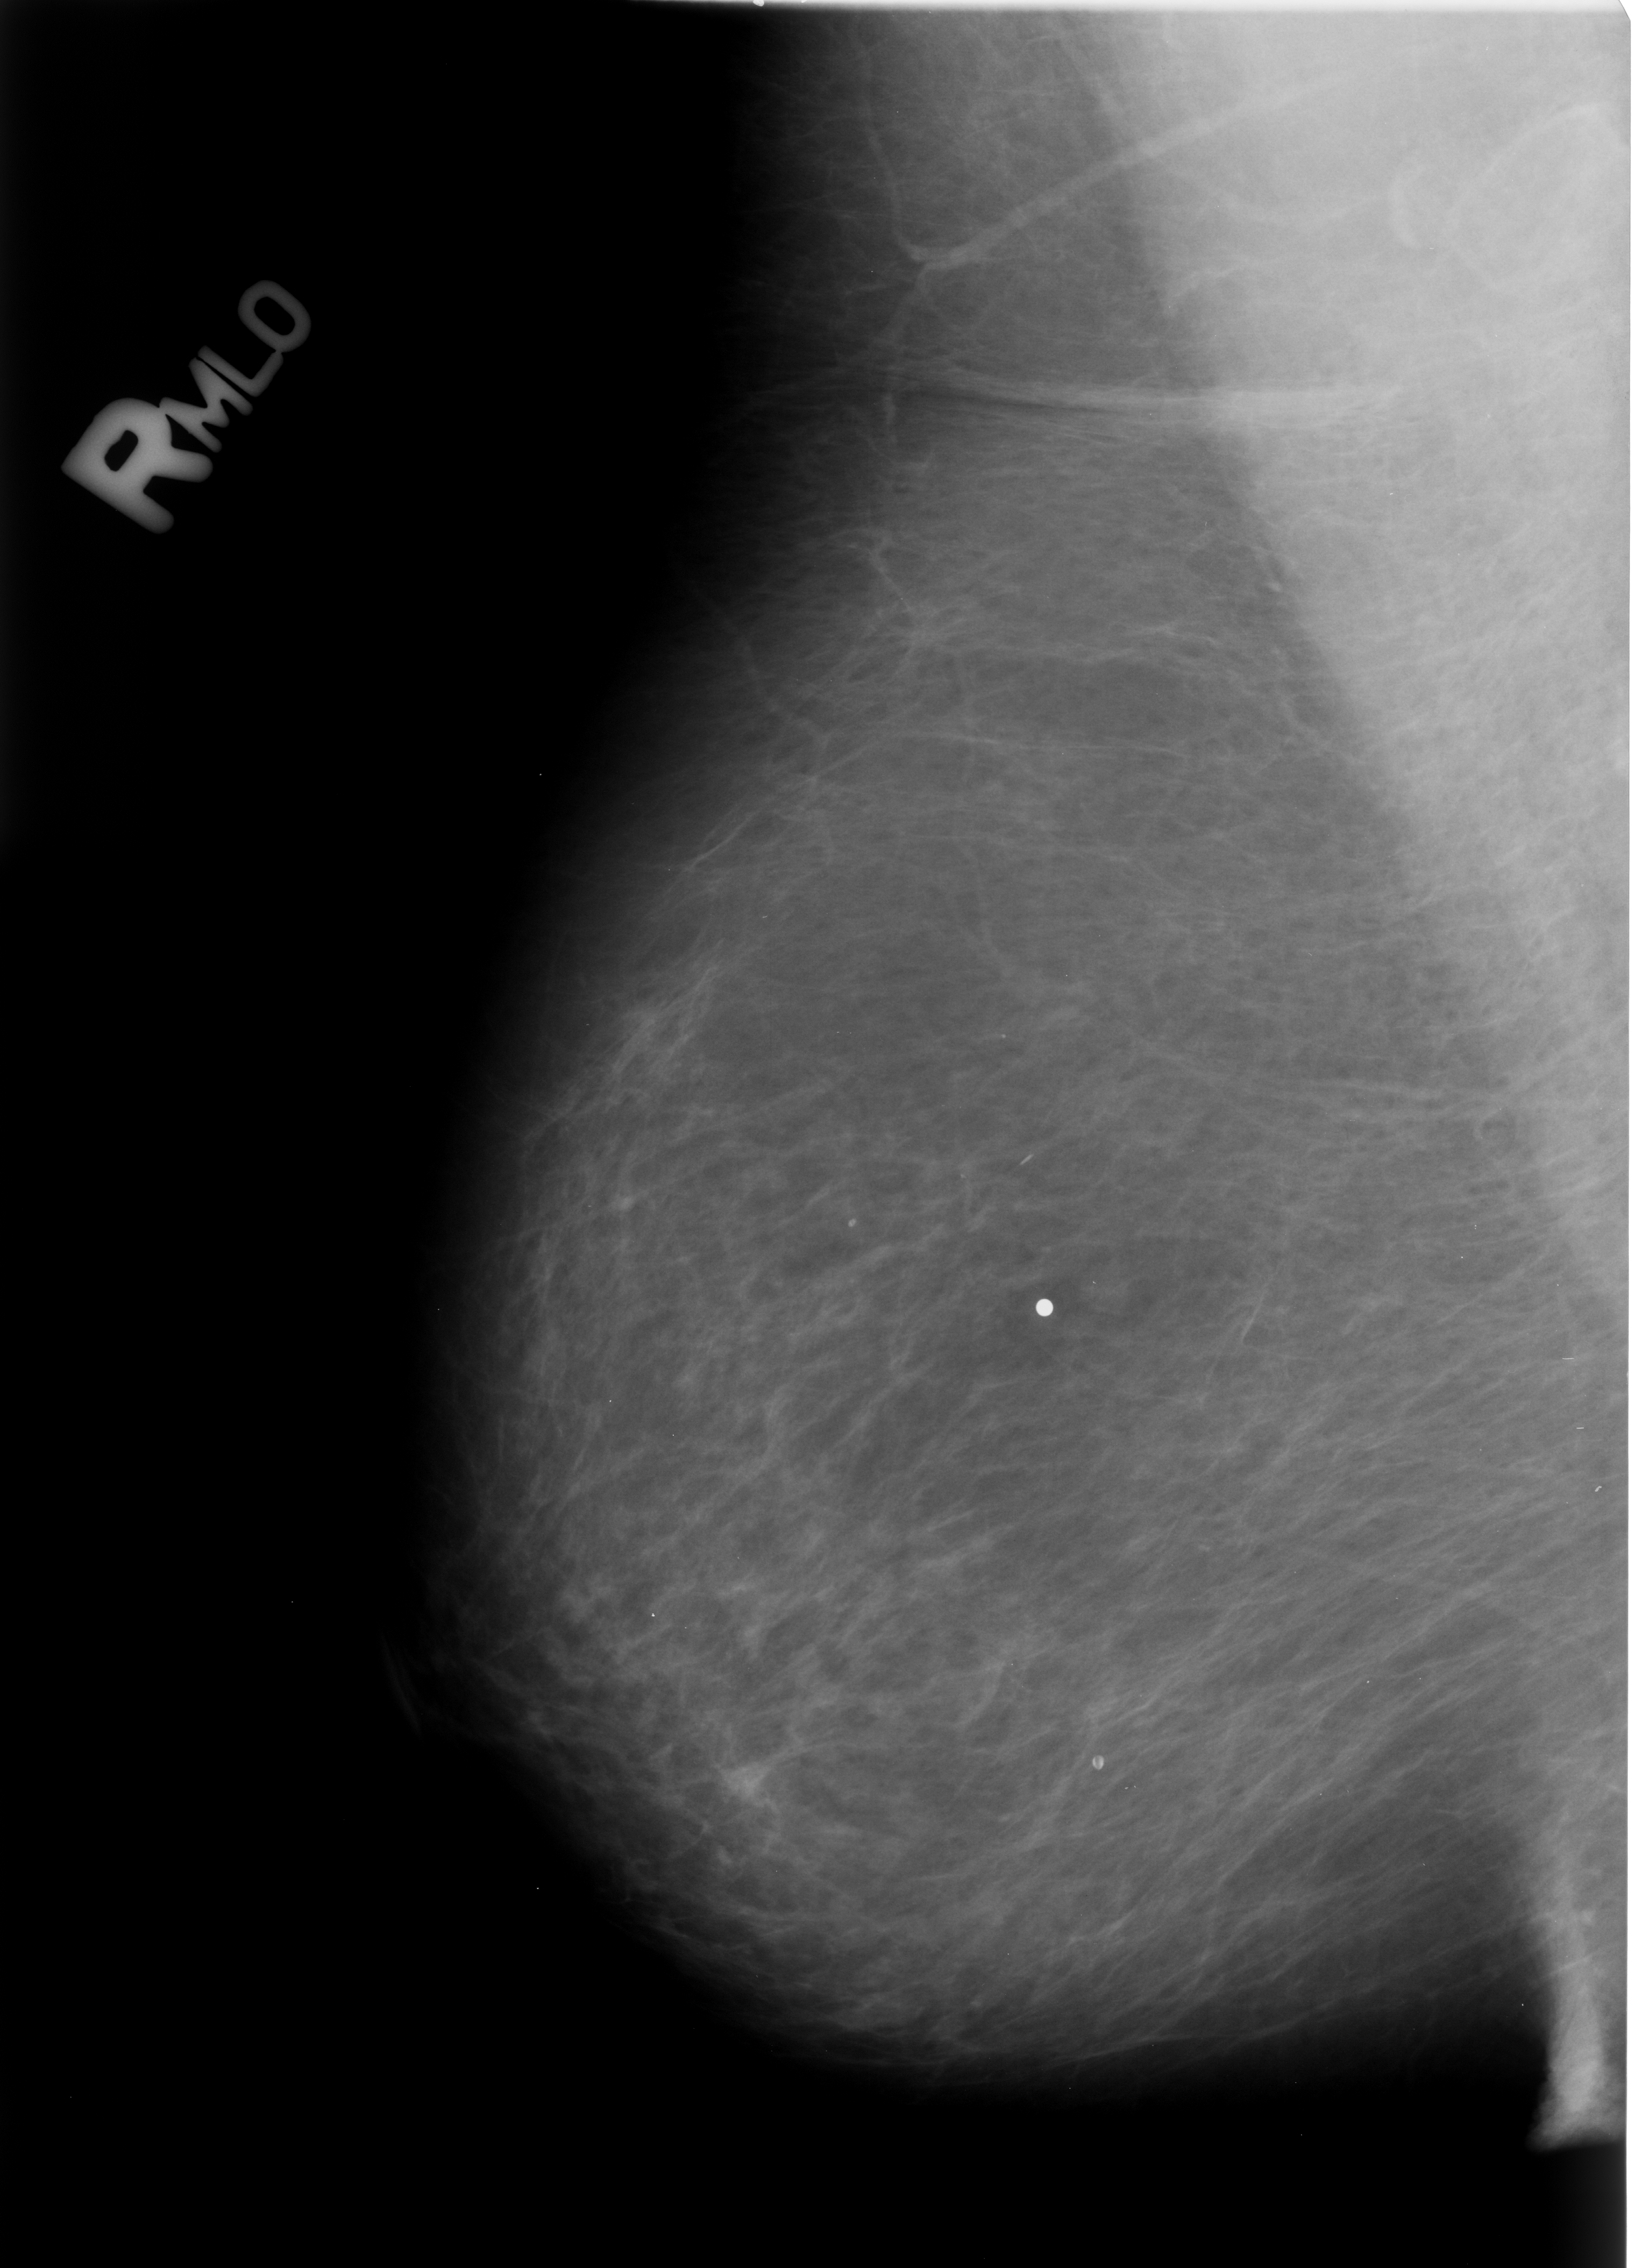
Scanned film-screen mammogram, right breast, mediolateral oblique (MLO) view, BI-RADS breast density category 1 (scale 1–4).
- Abnormality record for this image: Finding 1 of 2: calcifications, morphology lucent center; BI-RADS assessment category 2; subtlety rating 3 on a 1 (subtle) to 5 (obvious) scale; benign; no additional work-up was recommended (benign without callback).
- Finding 2 of 2: calcifications, morphology lucent center; BI-RADS assessment category 2; subtlety rating 3 on a 1 (subtle) to 5 (obvious) scale; benign without callback (not worked up further).